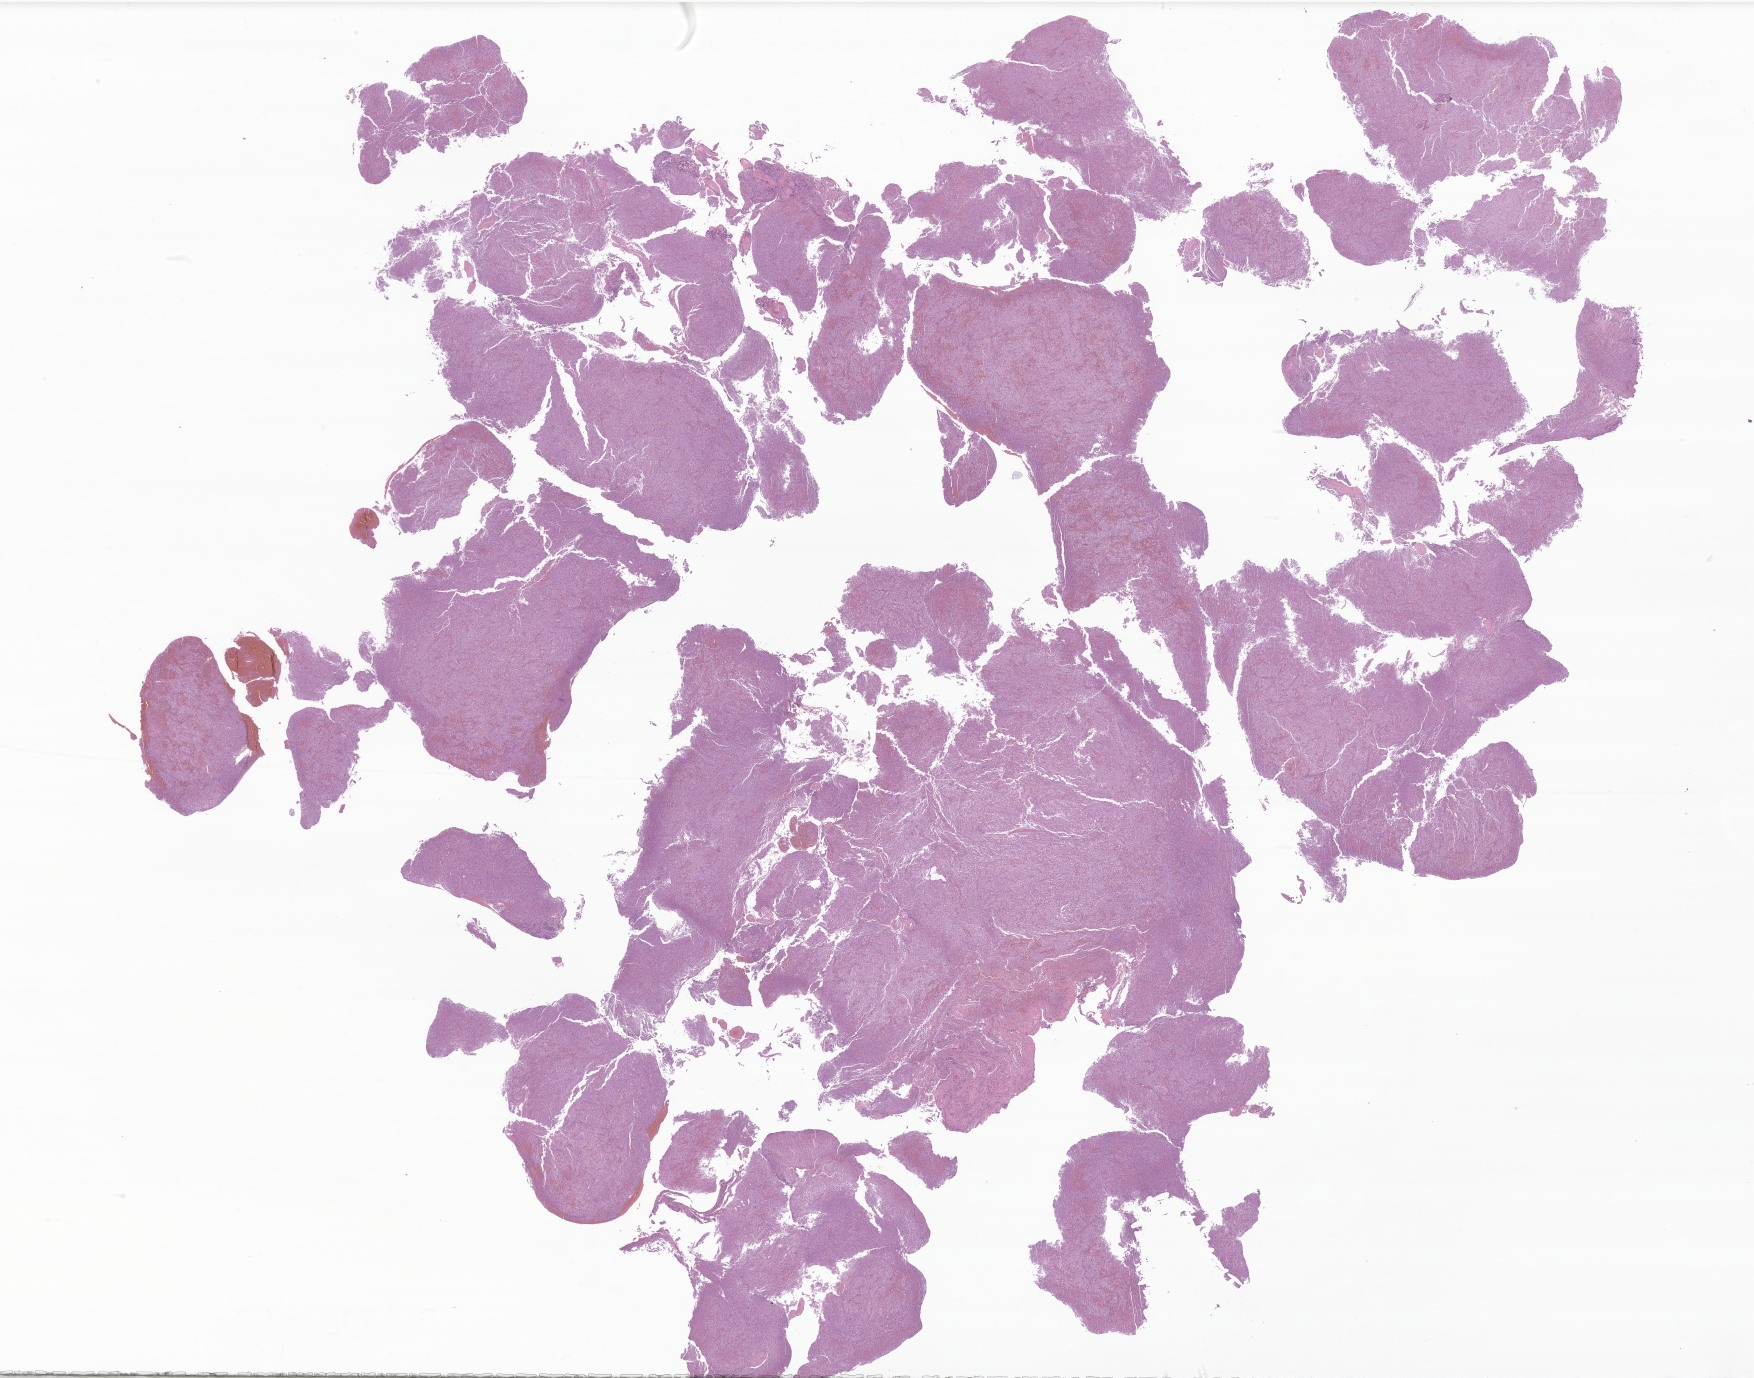
H&E whole-slide image of tumor tissue from the parietal lobe, whole scanned area (about 29.6 x 23.2 mm) shown as a low-resolution overview. Formalin-fixed, paraffin-embedded (FFPE) tissue. Patient: male, age 127 days.
Recorded diagnosis: Neoplasm, malignant.